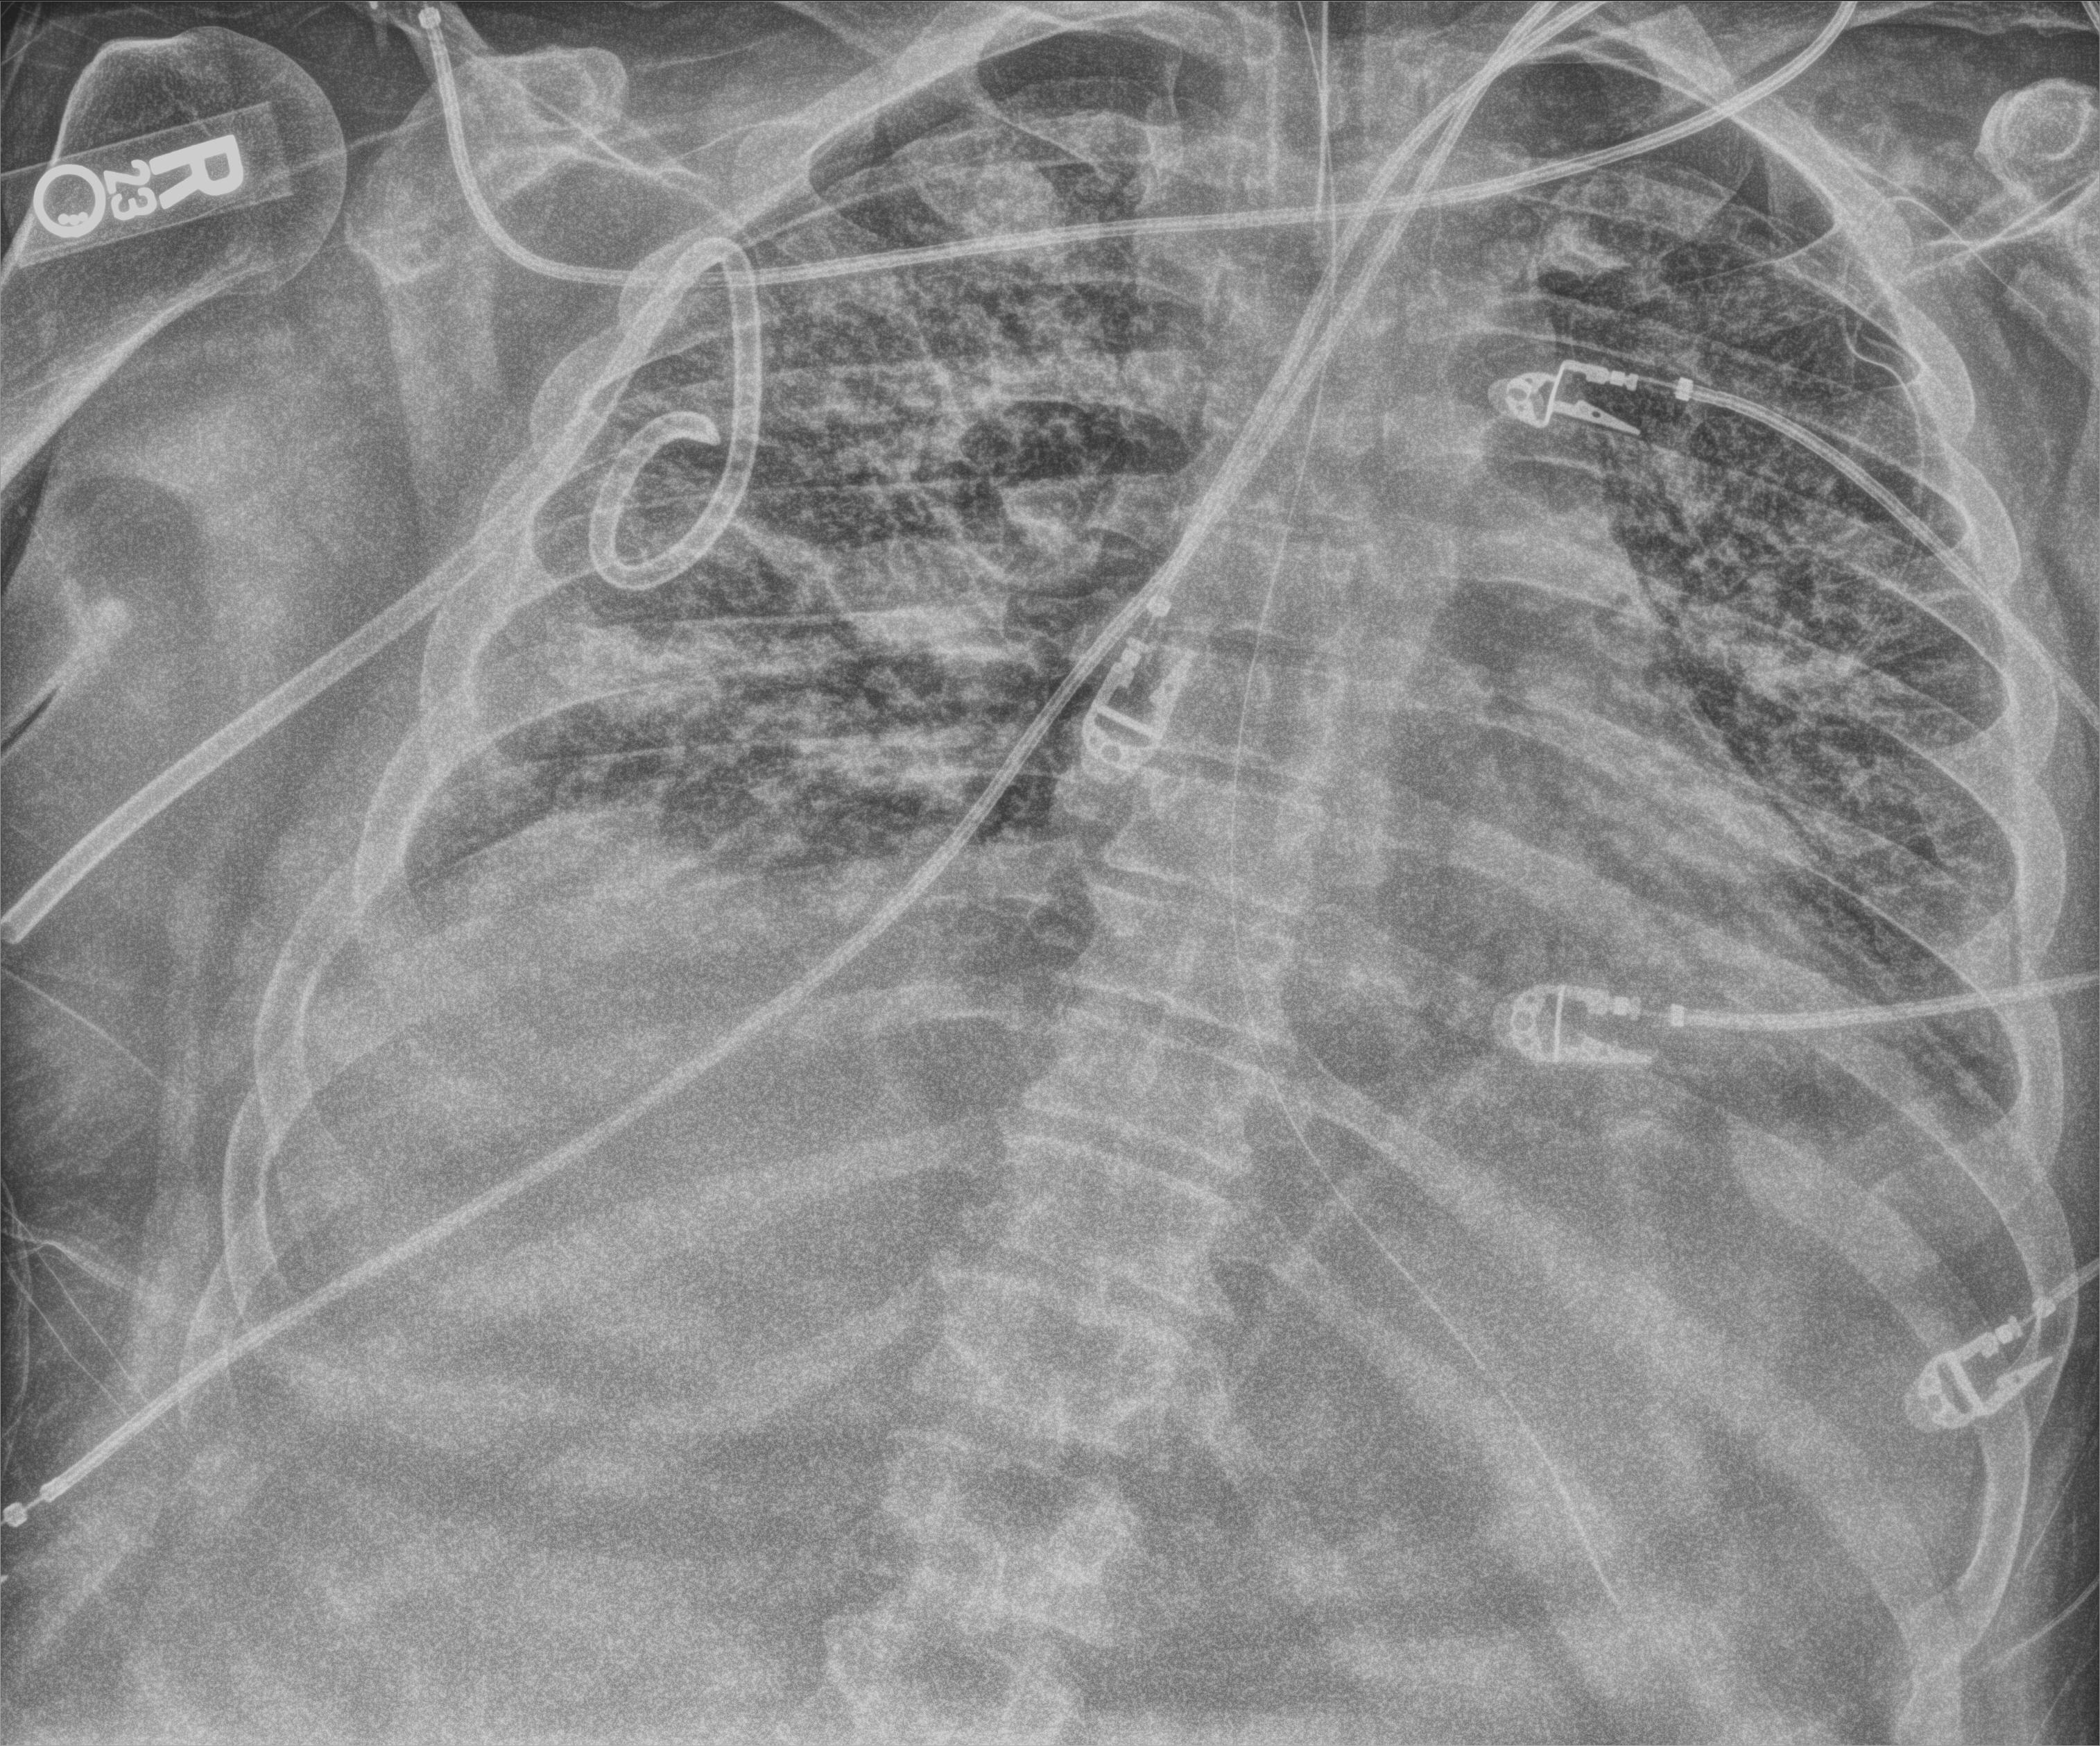
Chest X-ray (portable), anteroposterior (AP) projection. Patient hospitalised with COVID-19, aged 18–59 years.
From the hospital-stay record, not from the radiograph (when in the stay this image was taken is not recorded):
- length of hospital stay: 31 days
- mechanically ventilated during this hospital stay: yes